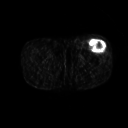
FDG PET of an extremity soft-tissue mass (from a PET/CT study), one axial slice; 128 × 128 image matrix, field of view 500 × 500 mm. Male patient, age 64 years. Case-level facts recorded for this patient, not image findings: histological type: extraskeletal osteosarcoma; grade: high; site of the primary tumour: thigh.
Annotated regions visible in this slice (expert contour drawn on MRI and transferred to this co-registered scan by the dataset authors):
- gross tumour volume (mass): bounding box (x1, y1, x2, y2) in pixels: (90, 40, 107, 53)